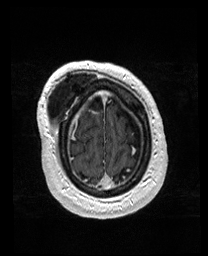
Brain MRI from a brain-tumour surgery series, one axial slice; position 34 of 176 along the scan axis; T1-weighted post-contrast; 1 mm slice thickness; 208 × 256 image matrix. From the clinical record (not read from this slice): histopathology: Astrocytoma; WHO grade: 4; IDH mutation: yes.
Structures marked on this image (manually delineated by an expert):
- previous resection cavity: bounding box [x1, y1, x2, y2] px = [56, 93, 106, 109]